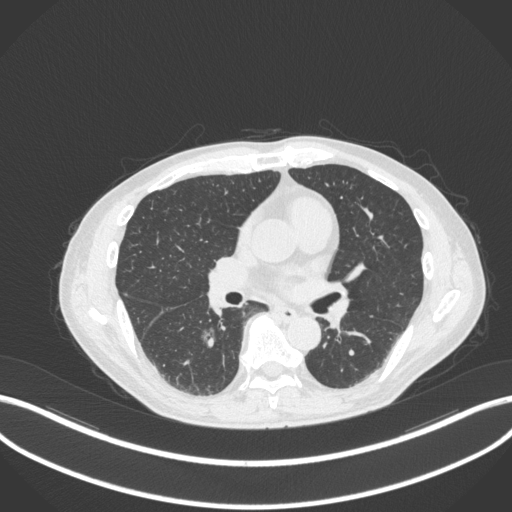
Chest CT, one axial slice. Position 167 of 324 along the scan axis. Reconstruction kernel B31f. 120 kVp. Lung window (W 1500 / L -600 HU). 1 mm slice thickness. 512 × 512 image matrix. Patient: male, 61 years. Case-level facts recorded for this patient, not image findings: clinical TNM (as recorded): T1c N0 M0.
Annotated regions visible in this slice (rectangle marked by the reading radiologist):
- lung tumour (recorded histology: adenocarcinoma): bounding box [x1, y1, x2, y2] px = [194, 316, 220, 352]